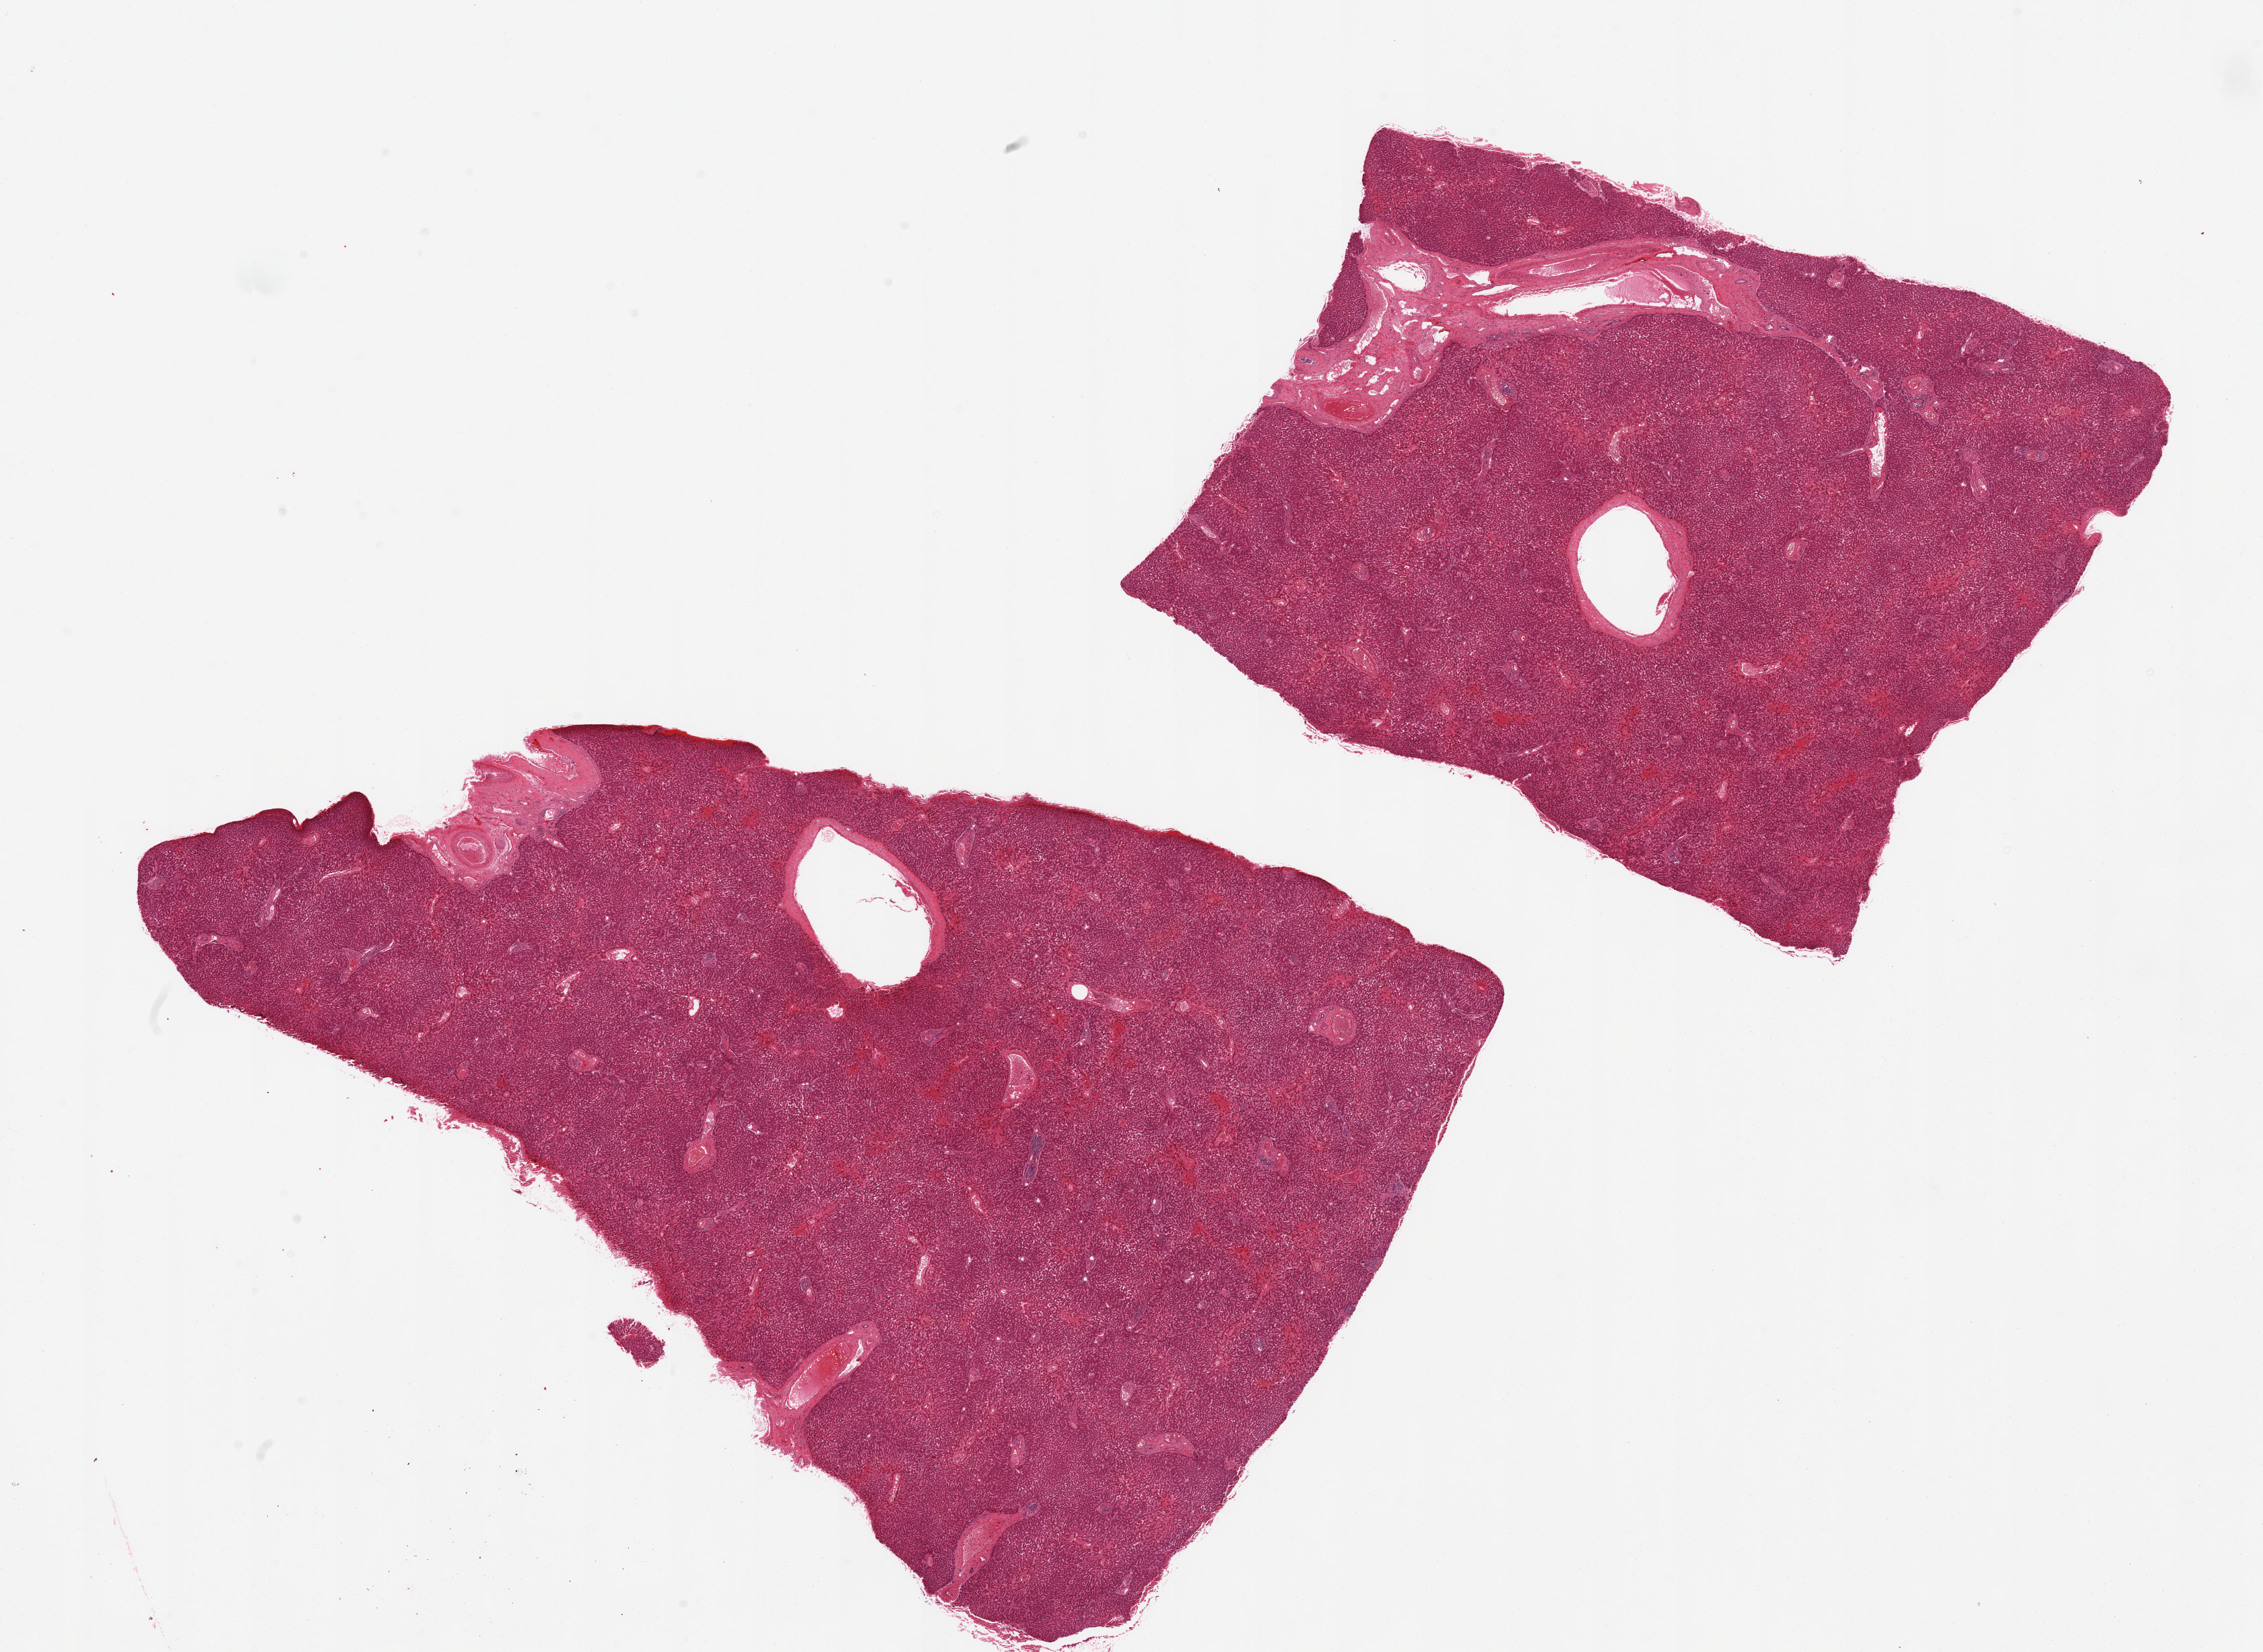
Digitized hematoxylin and eosin (H&E)-stained section, brightfield — shown as a low-resolution overview of the whole scanned area (about 26.6 x 19.4 mm), PAXgene-fixed paraffin-embedded (PFPE) section, target tissue: liver, tissue donor sample. Female donor.
Review note (as recorded): 2 pieces; central vascular congestion.